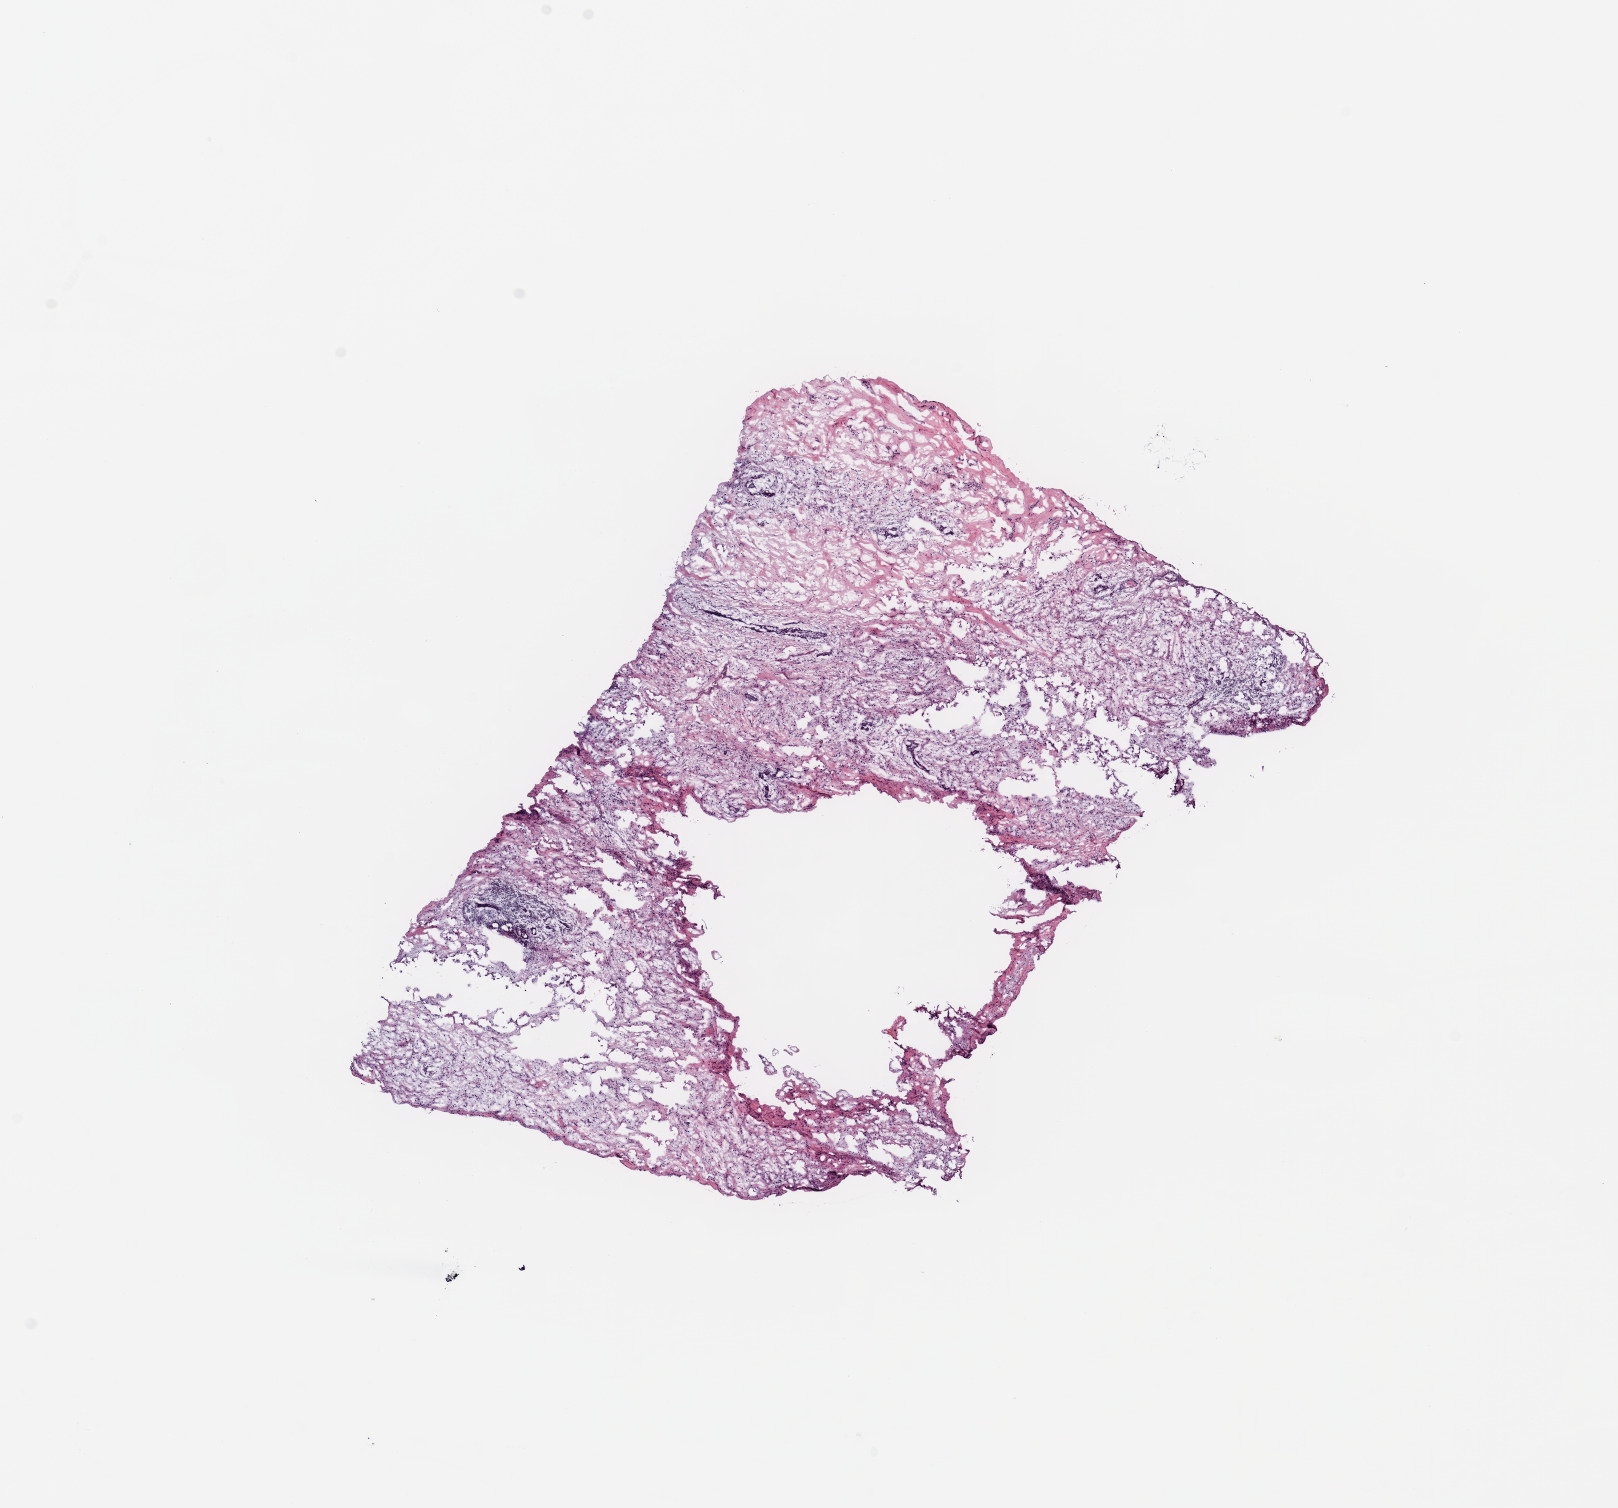
Whole-slide histology image, Hematoxylin and eosin (H&E) stained, low-resolution overview of the scanned area, about 12.8 x 11.9 mm; breast, tissue type not recorded.
Patient diagnosis (cohort enrolment): breast cancer (breast).